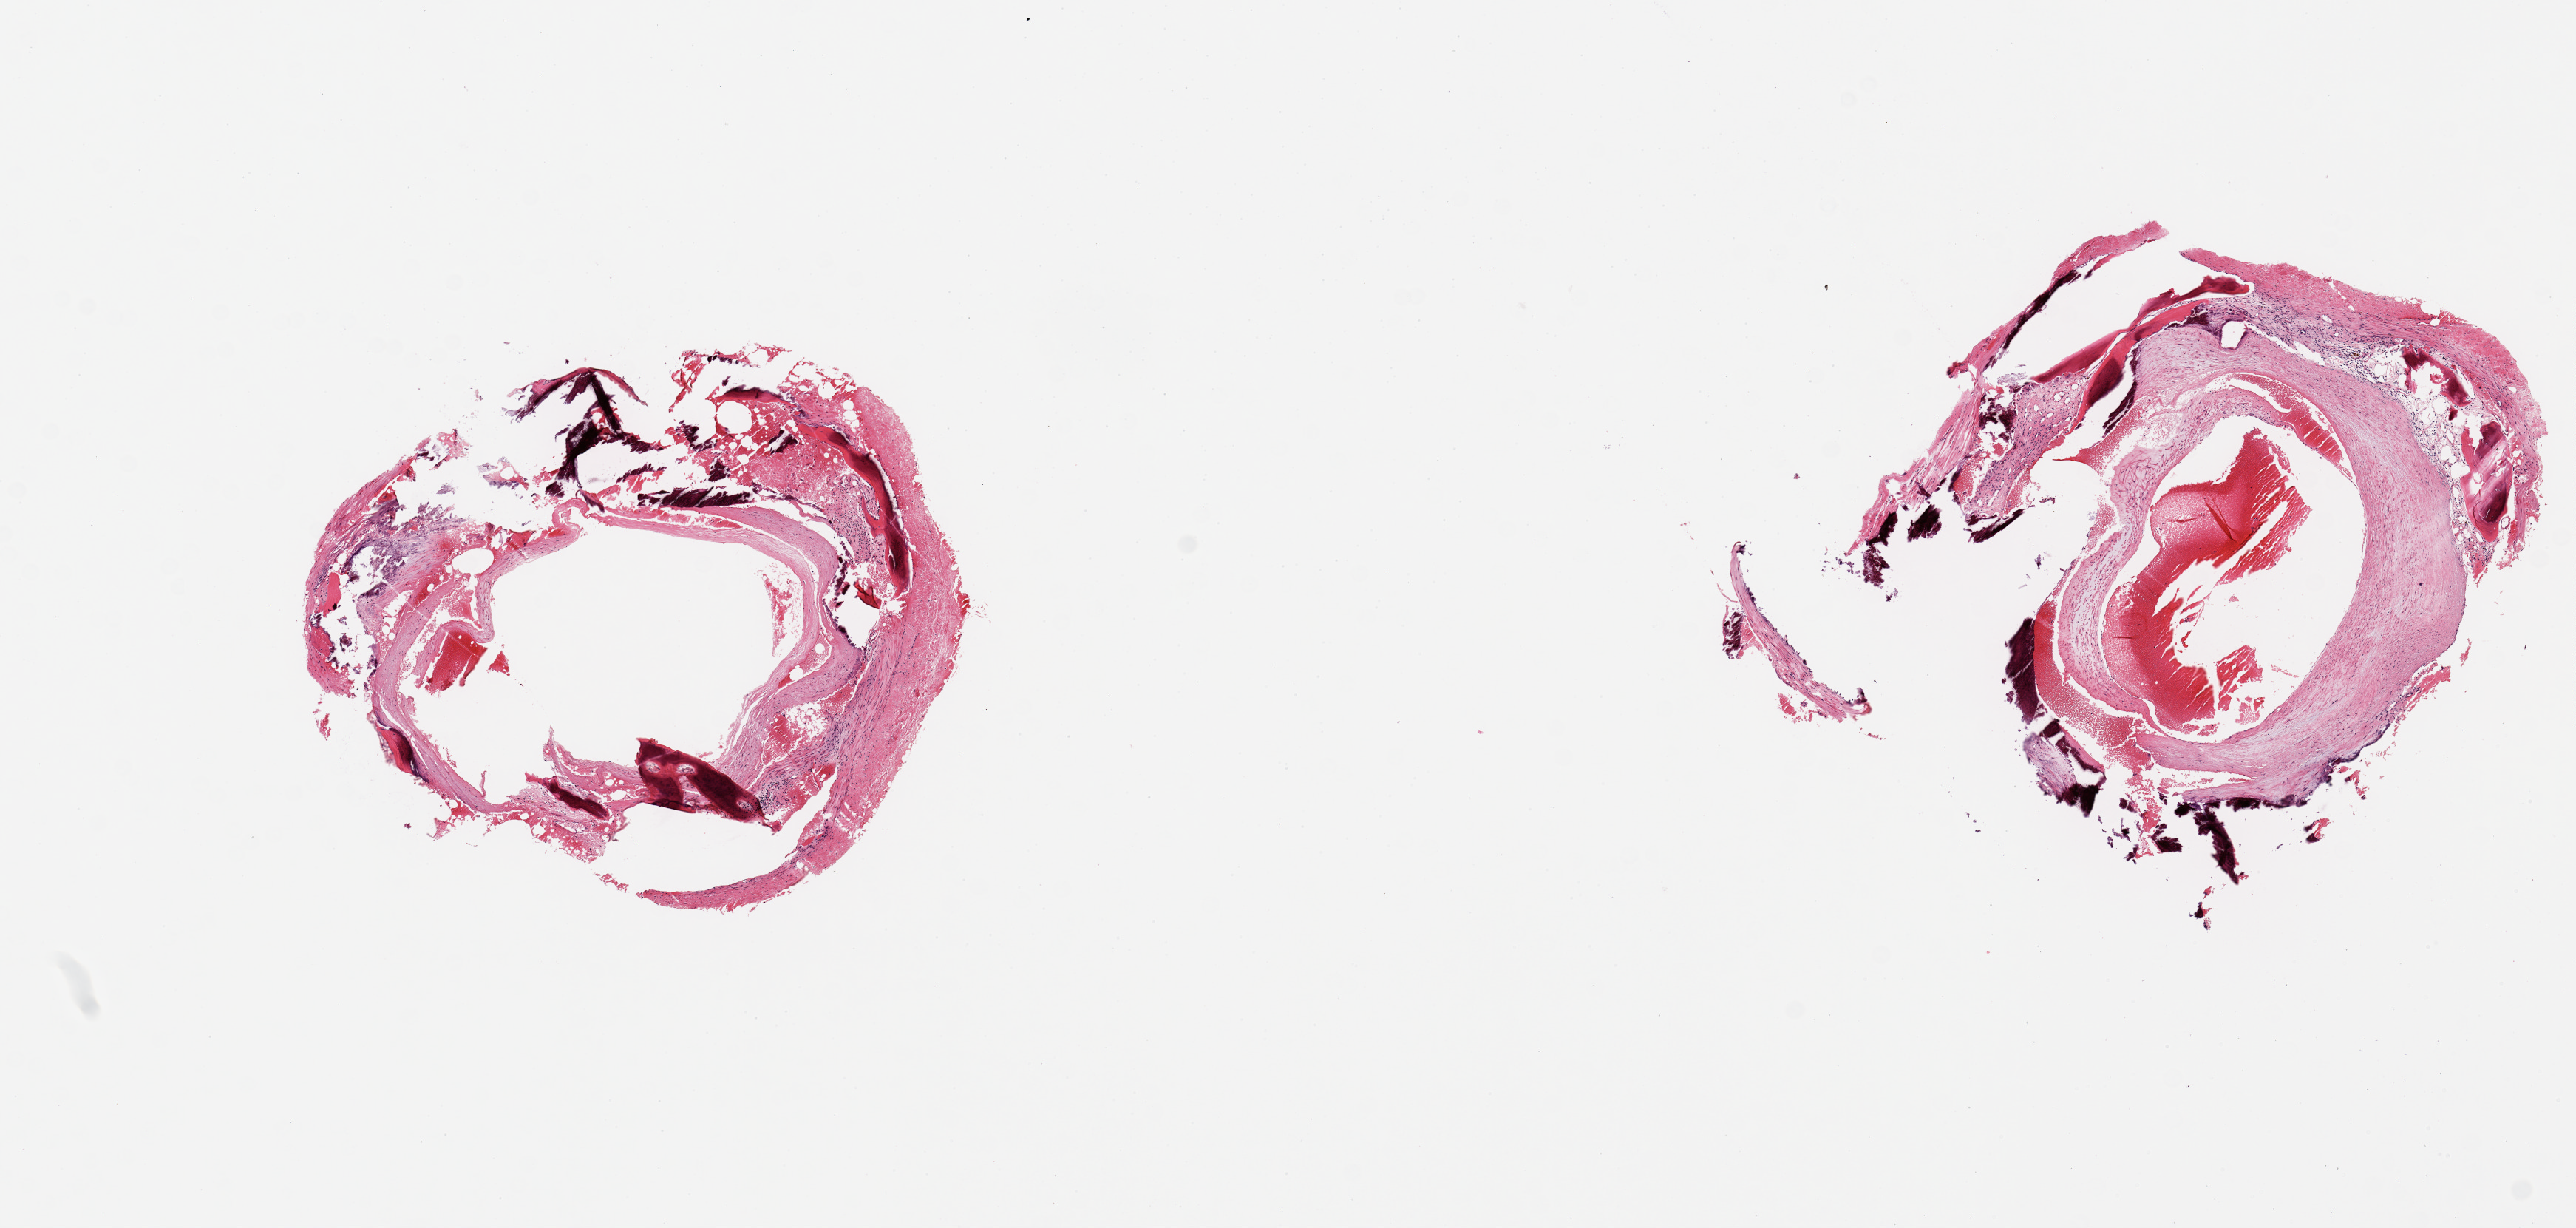
Hematoxylin and eosin (H&E) whole-slide image, brightfield — low-resolution overview of the scanned area, about 13.8 x 6.6 mm. PAXgene-fixed, paraffin-embedded tissue. Target tissue: tibial artery. Donor tissue sample. Male donor.
Pathologist's review note for this sample: 2 pieces, extensive dystrophic calcification, Monckeberg sclerosis, minimal atherosis.